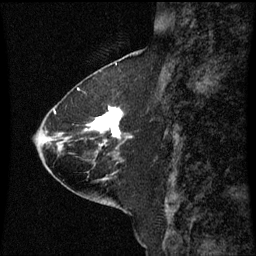
Breast MRI (dynamic contrast-enhanced), one sagittal slice. Position 25 of 60 along the scan axis. Dynamic contrast-enhanced series, image 2 of 3 at this slice position (ordered by acquisition). 1.5 T. TE 4.2 ms, TR 8.9 ms. 256 × 256 image matrix, field of view 200 × 200 mm. Patient: female, 63 years. From the clinical record (not read from this slice): setting: breast cancer imaged before/during neoadjuvant chemotherapy; receptor status: HR-positive, HER2-negative.
Outlined on this slice (semi-automatically segmented with operator editing):
- analysis volume of interest (the breast-tissue region the enhancement analysis was run in; not a lesion): bounding box (x1, y1, x2, y2) in pixels: (84, 106, 131, 151)
- tumour enhancement mask (voxels above the 70 % enhancement threshold inside the analysis volume of interest): (90, 106, 122, 145)